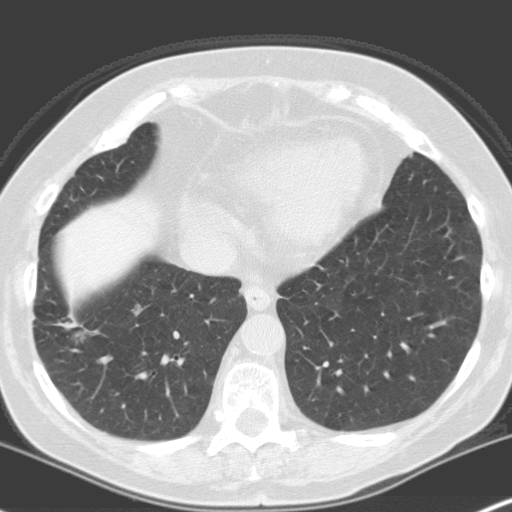
Low-dose screening chest CT, one axial slice; slice 59 of 160 in the series (ordered by position); lung window (W 1500 / L -600 HU); 3.2 mm slice thickness; 512 × 512 image matrix, field of view 316 × 316 mm.
Structures marked on this image (manually delineated by an expert):
- lesion 1 (tumor, lower lobe of right lung): bounding box (x1, y1, x2, y2) in pixels: (62, 323, 87, 338)